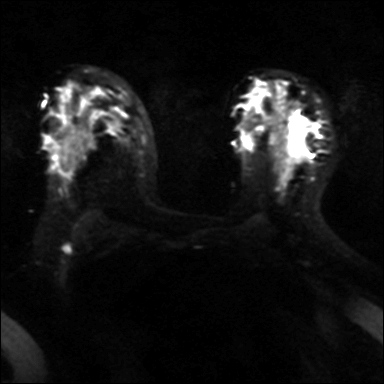
Breast MRI, one axial slice. Position 24 of 40 along the scan axis. Diffusion-weighted series; image 2 of 4 stored at this slice position (different b-values; order by instance number). 3 T. 4 mm slice thickness. 384 × 384 image matrix. Female patient.
Outlined on this slice (manually delineated by an expert):
- tumour on diffusion-weighted imaging: bounding box (x1, y1, x2, y2) in pixels: (294, 123, 305, 141)